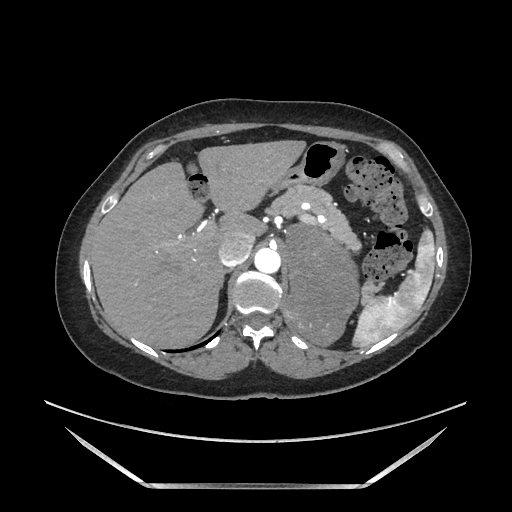
Contrast-enhanced abdominal CT, one axial slice; slice 127 of 205 in the series (ordered by position); soft-tissue window (W 400 / L 40 HU); 512 × 512 image matrix, field of view 440 × 440 mm. Female patient. Case-level facts recorded for this patient, not image findings: diagnosis: adrenocortical carcinoma; tumour side: left adrenal; tumour size at pathology: 12.5 cm; Ki-67 index: 39 %; stage (as recorded): 3.
Outlined on this slice (semi-automatic segmentation, software-assisted and operator-edited):
- mass: bounding box [x1, y1, x2, y2] px = [287, 224, 361, 344]